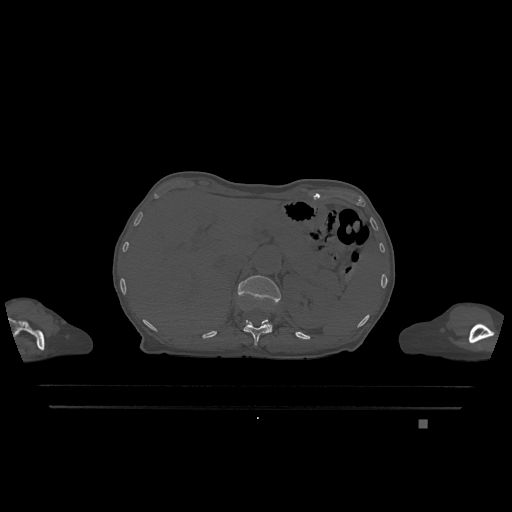
CT including the spine, one axial slice; slice 512 of 1317 in the series (ordered by position); bone window (W 1800 / L 400 HU); 0.5 mm slice thickness; 512 × 512 image matrix, field of view 500 × 500 mm. Patient: female, 74 years. Case-level facts recorded for this patient, not image findings: primary cancer: lung.
Outlined on this slice (semi-automatic segmentation, software-assisted and operator-edited):
- L1 vertebra: bounding box [x1, y1, x2, y2] px = [238, 275, 281, 331]
- T12 vertebra: [244, 320, 271, 346]